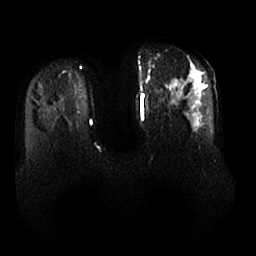
Breast MRI, one axial slice; slice 12 of 25 in the series (ordered by position); diffusion-weighted series; image 2 of 4 stored at this slice position (different b-values; order by instance number); 1.5 T; 4 mm slice thickness; 256 × 256 image matrix, field of view 380 × 380 mm. Female patient.
Outlined on this slice (manually delineated by an expert):
- tumour on diffusion-weighted imaging: bounding box (x1, y1, x2, y2) in pixels: (189, 74, 195, 78)